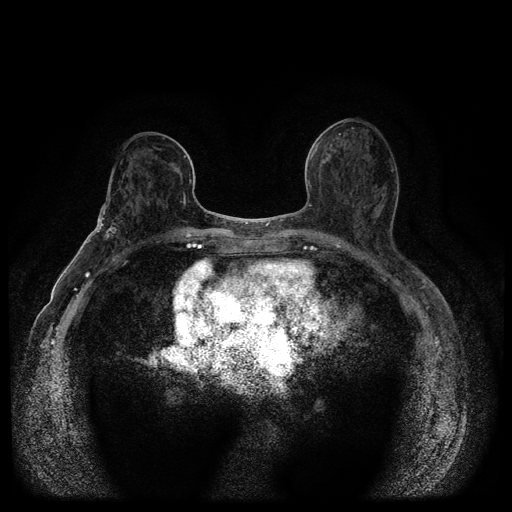
Breast MRI (dynamic contrast-enhanced, multi-phase), one axial slice; position 50 of 116 along the scan axis; dynamic contrast-enhanced series, time point 2 of 5 at this slice position (early post-contrast); 1.5 T; TE 2.7 ms, TR 5.4 ms; 2 mm slice thickness; 512 × 512 image matrix. Female patient, age 75 years.
Annotated regions visible in this slice (semi-automatically segmented with operator editing):
- breast lesion (labelled 'tumour' in the annotation; benign lesions carry a separate 'benign' label): box from (x=86, y=208) to (x=122, y=245) px